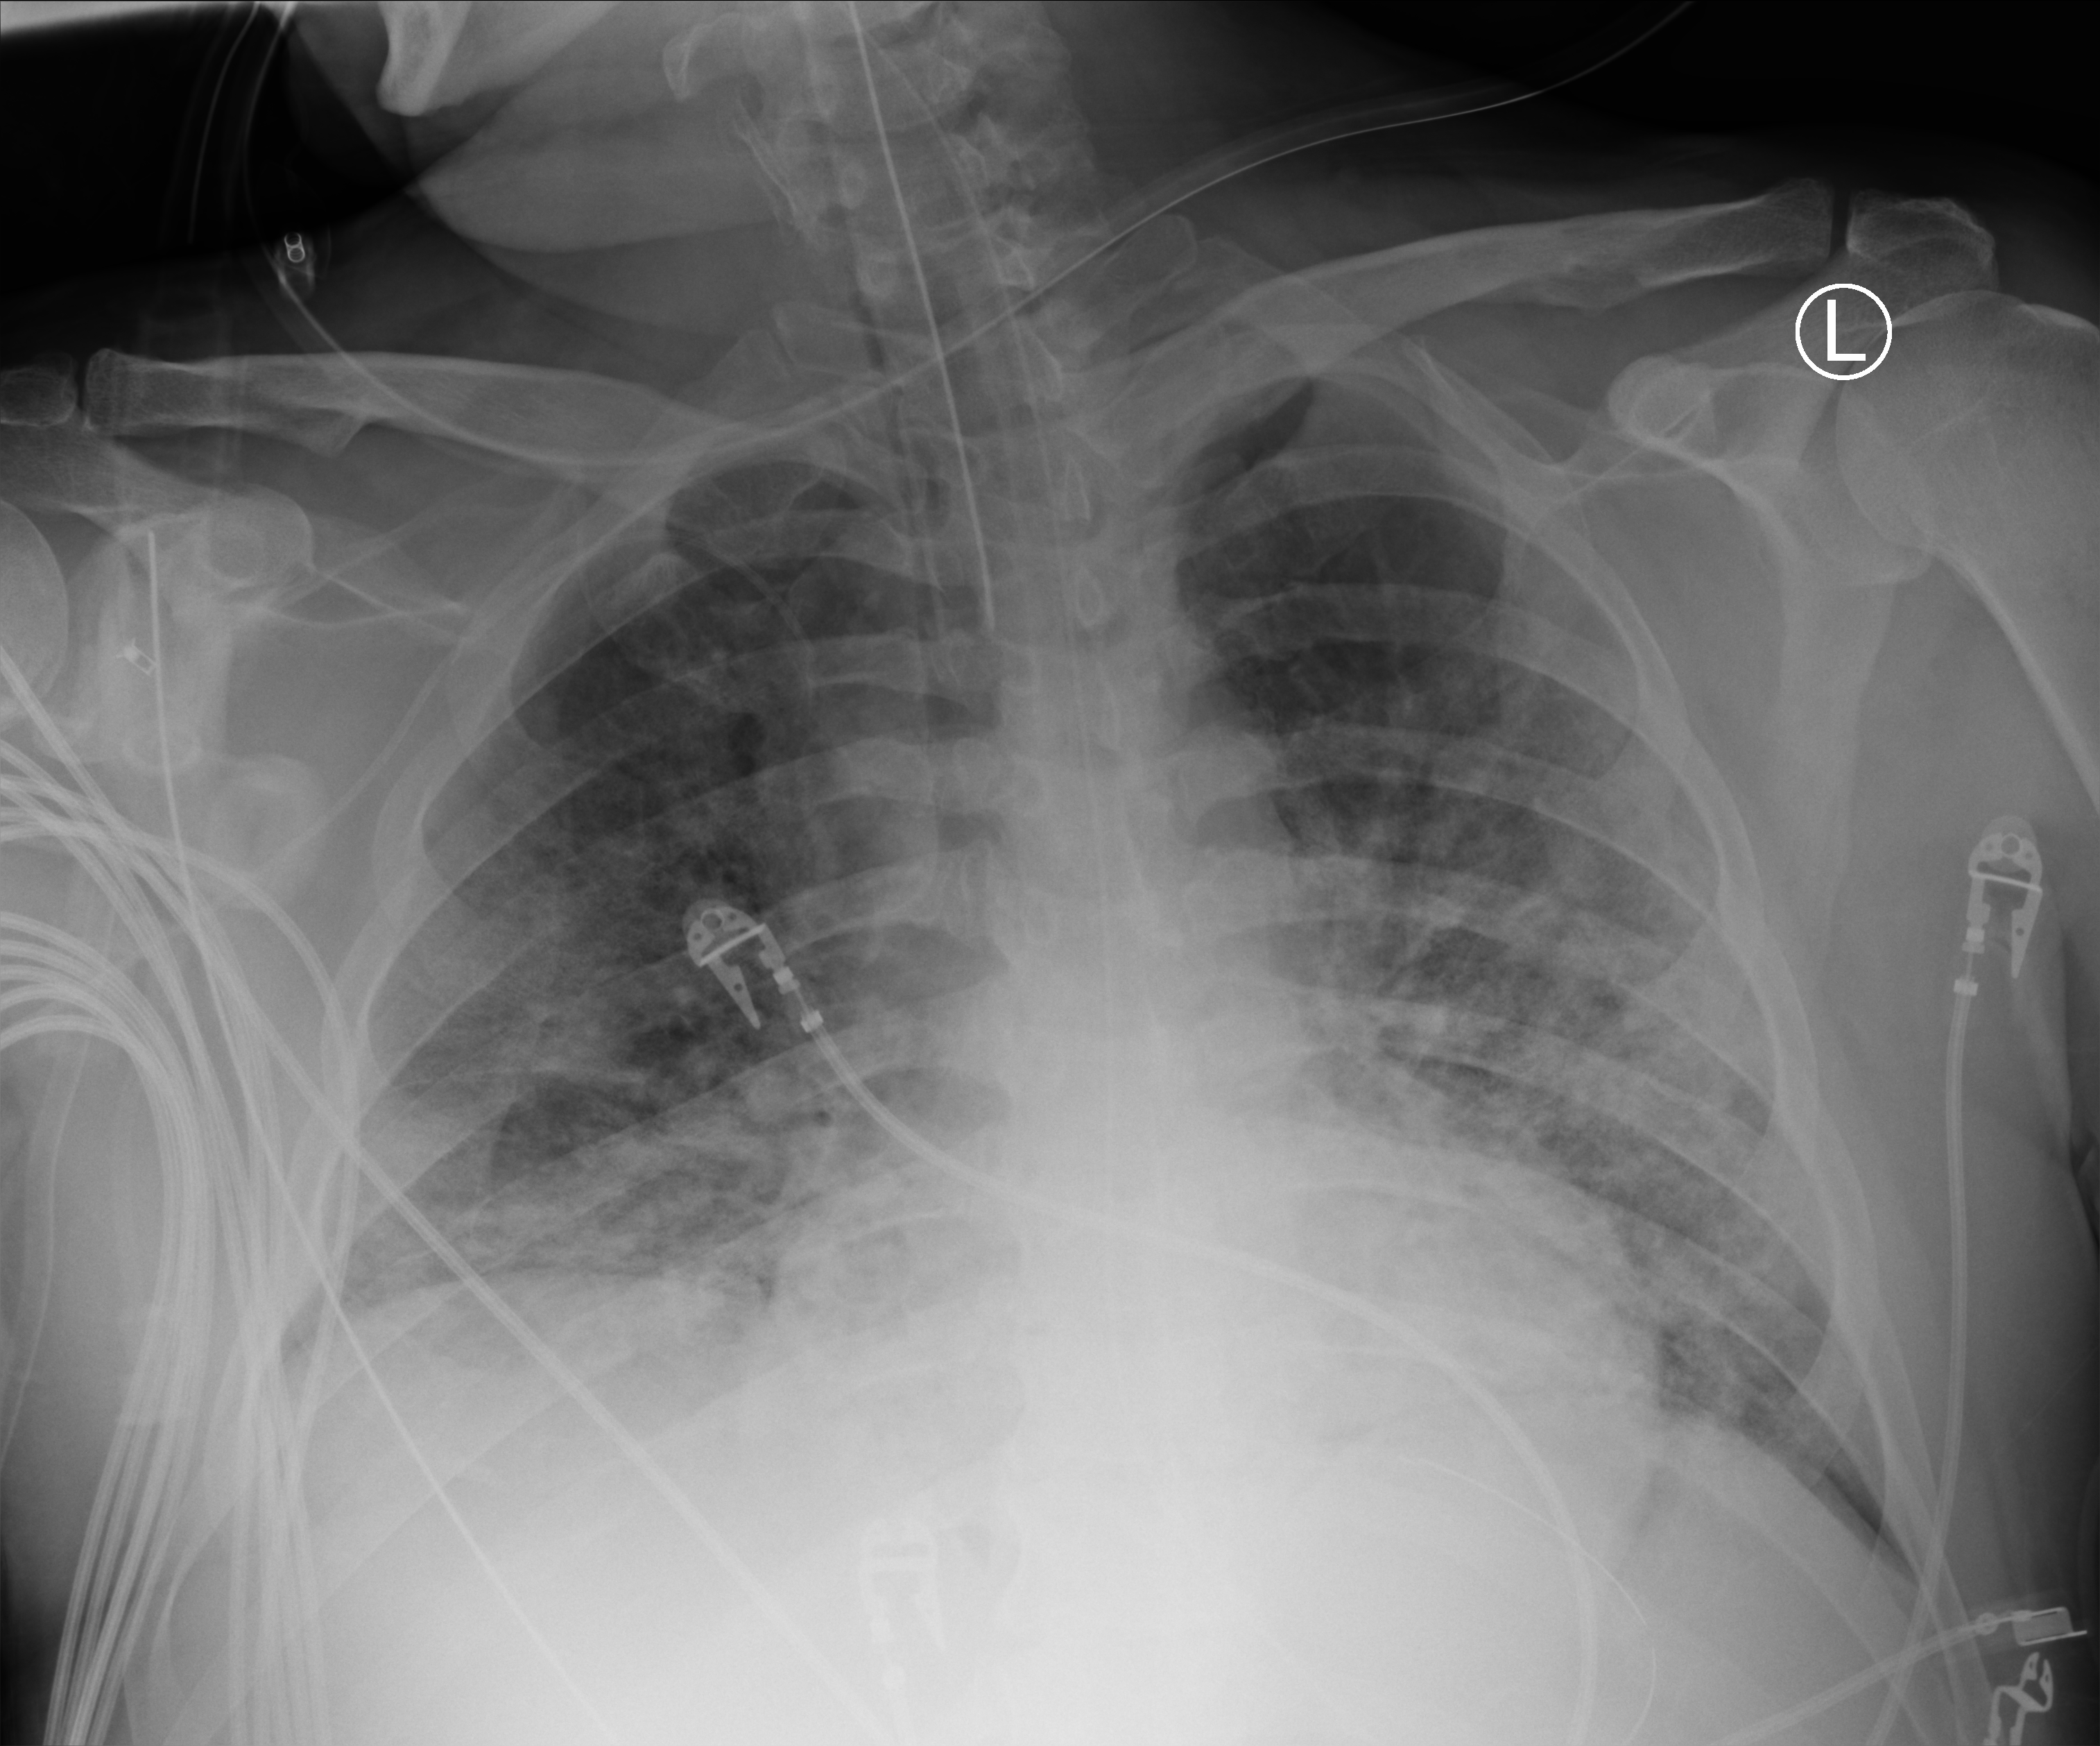
Portable chest radiograph, anteroposterior (AP) projection. Patient hospitalised with COVID-19; male, aged 18–59 years.
From the hospital-stay record, not from the radiograph (when in the stay this image was taken is not recorded): admitted to intensive care during this hospital stay: yes; chronic kidney disease (admission record): no; COPD (admission record): no.